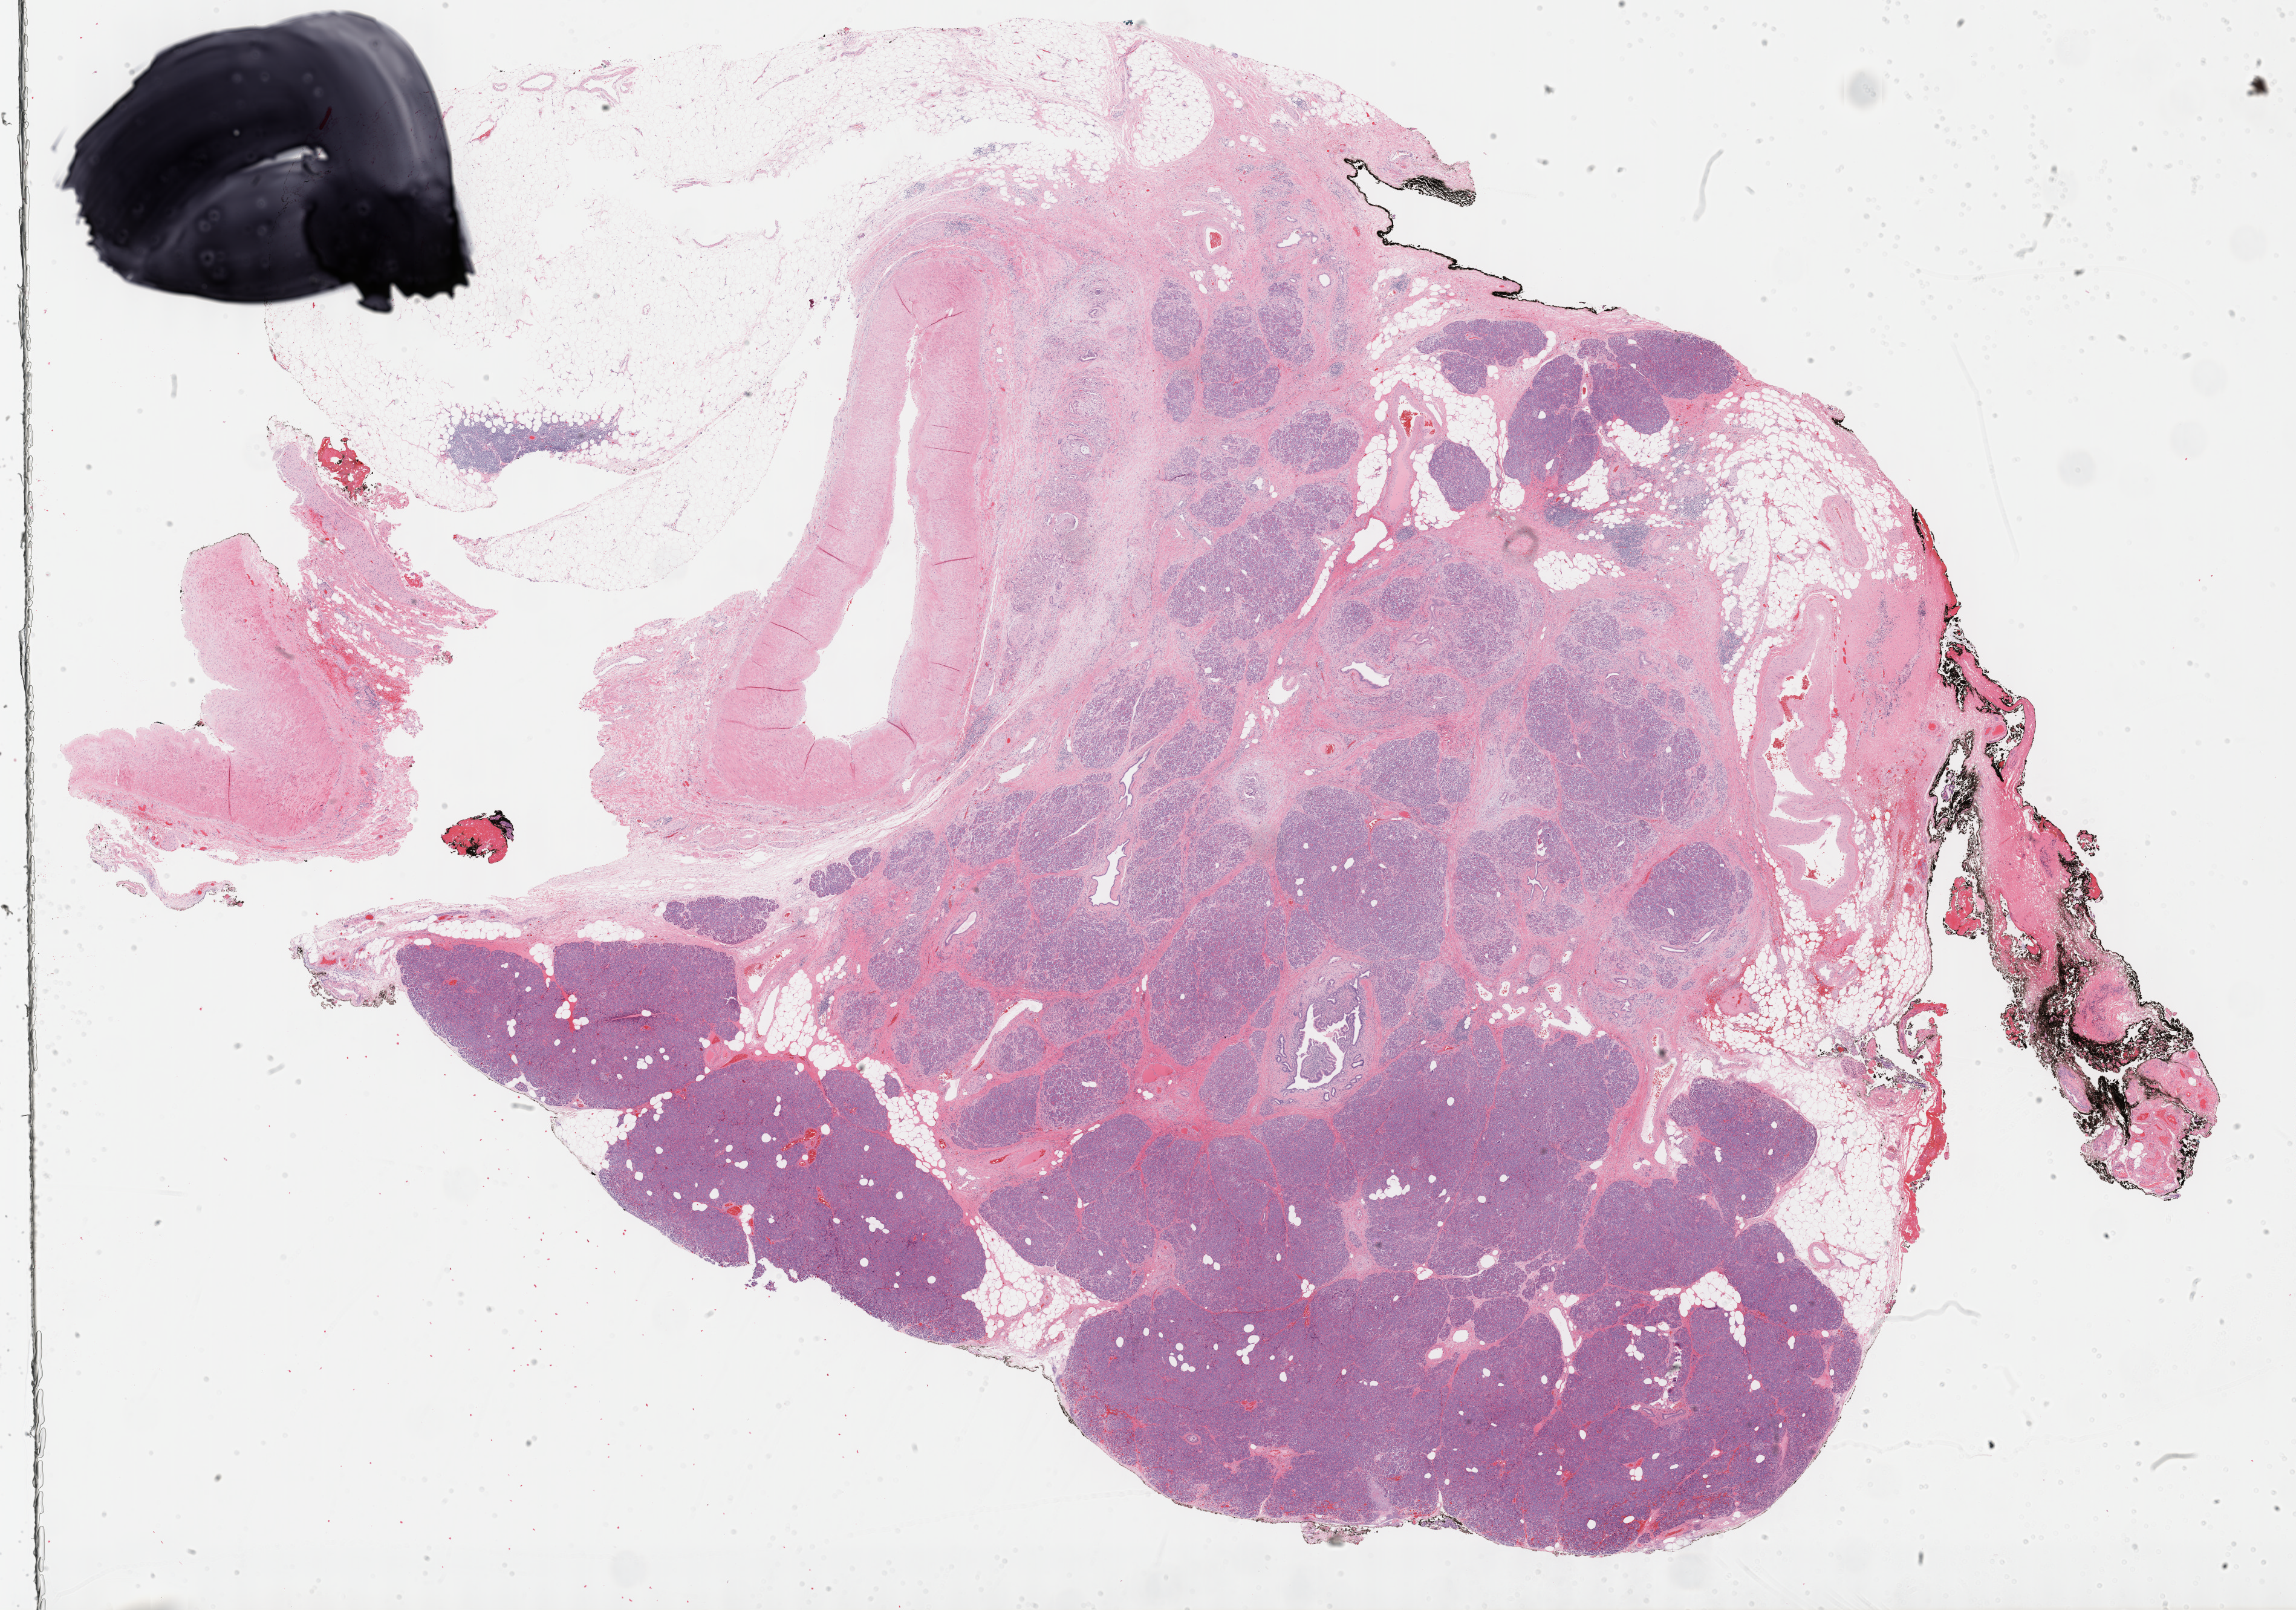
Digitized H&E tissue section (whole slide), a low-resolution overview of the entire scanned area, about 30.7 x 21.5 mm (slide scanned at 40x). Formalin-fixed paraffin-embedded (FFPE) diagnostic section. Pancreas, primary tumour sample. Female patient; age at initial diagnosis 66 years. Histologic grade: G2 (moderately differentiated).
Histologic diagnosis: Infiltrating duct carcinoma, NOS (body of pancreas). AJCC pathologic stage: IV (7th edition). Lymph nodes positive (case pathology): 1 of 12 examined.